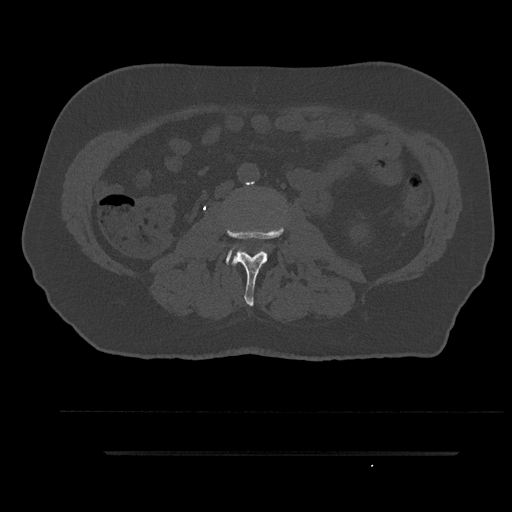
CT including the spine, one axial slice; slice 84 of 797 in the series (ordered by position); reconstruction kernel Br40s/3; 120 kVp; bone window (W 1800 / L 400 HU); 0.5 mm slice thickness; 512 × 512 image matrix, field of view 432 × 432 mm. Patient: male, 63 years. Case-level facts recorded for this patient, not image findings: primary cancer: renal; vertebrae with lytic lesions (as recorded): T8.
Outlined on this slice (semi-automatic segmentation, software-assisted and operator-edited):
- L2 vertebra: bounding box [x1, y1, x2, y2] px = [225, 226, 284, 306]
- L3 vertebra: [226, 250, 242, 265]